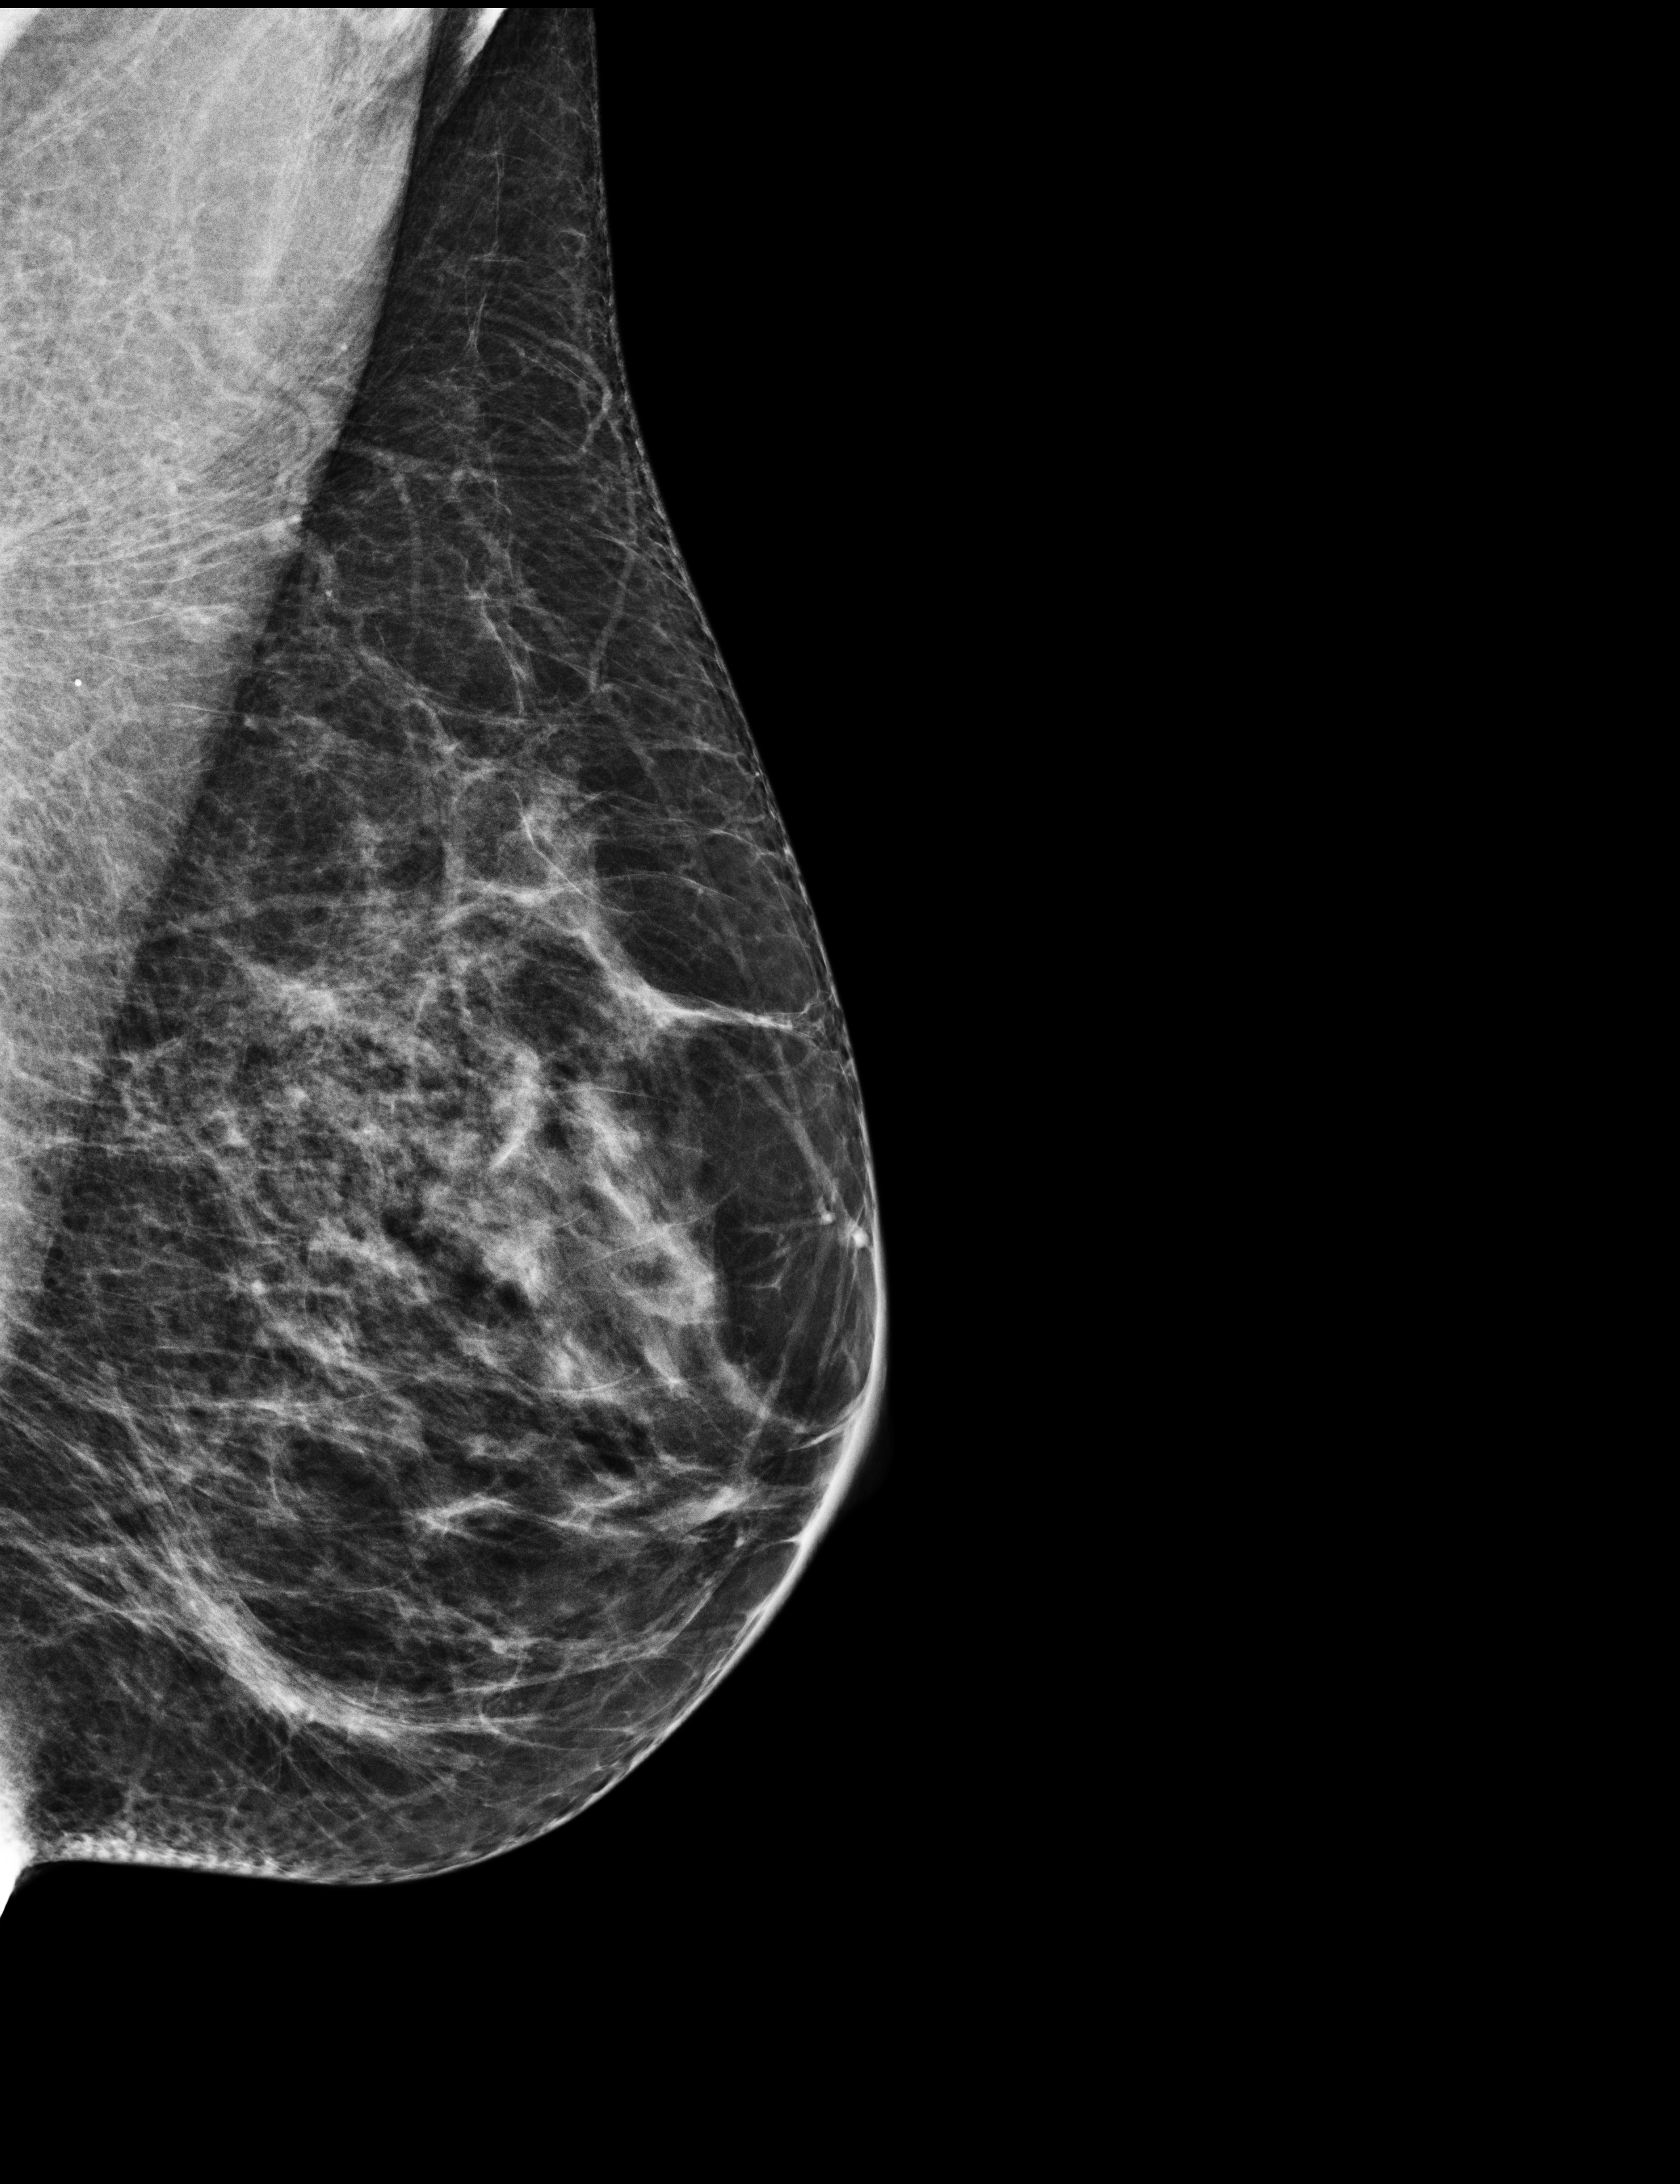
Screening examination; system: Selenia Dimensions.
Image type: full-field digital mammogram. Breast: left. Projection: medio-lateral oblique projection.